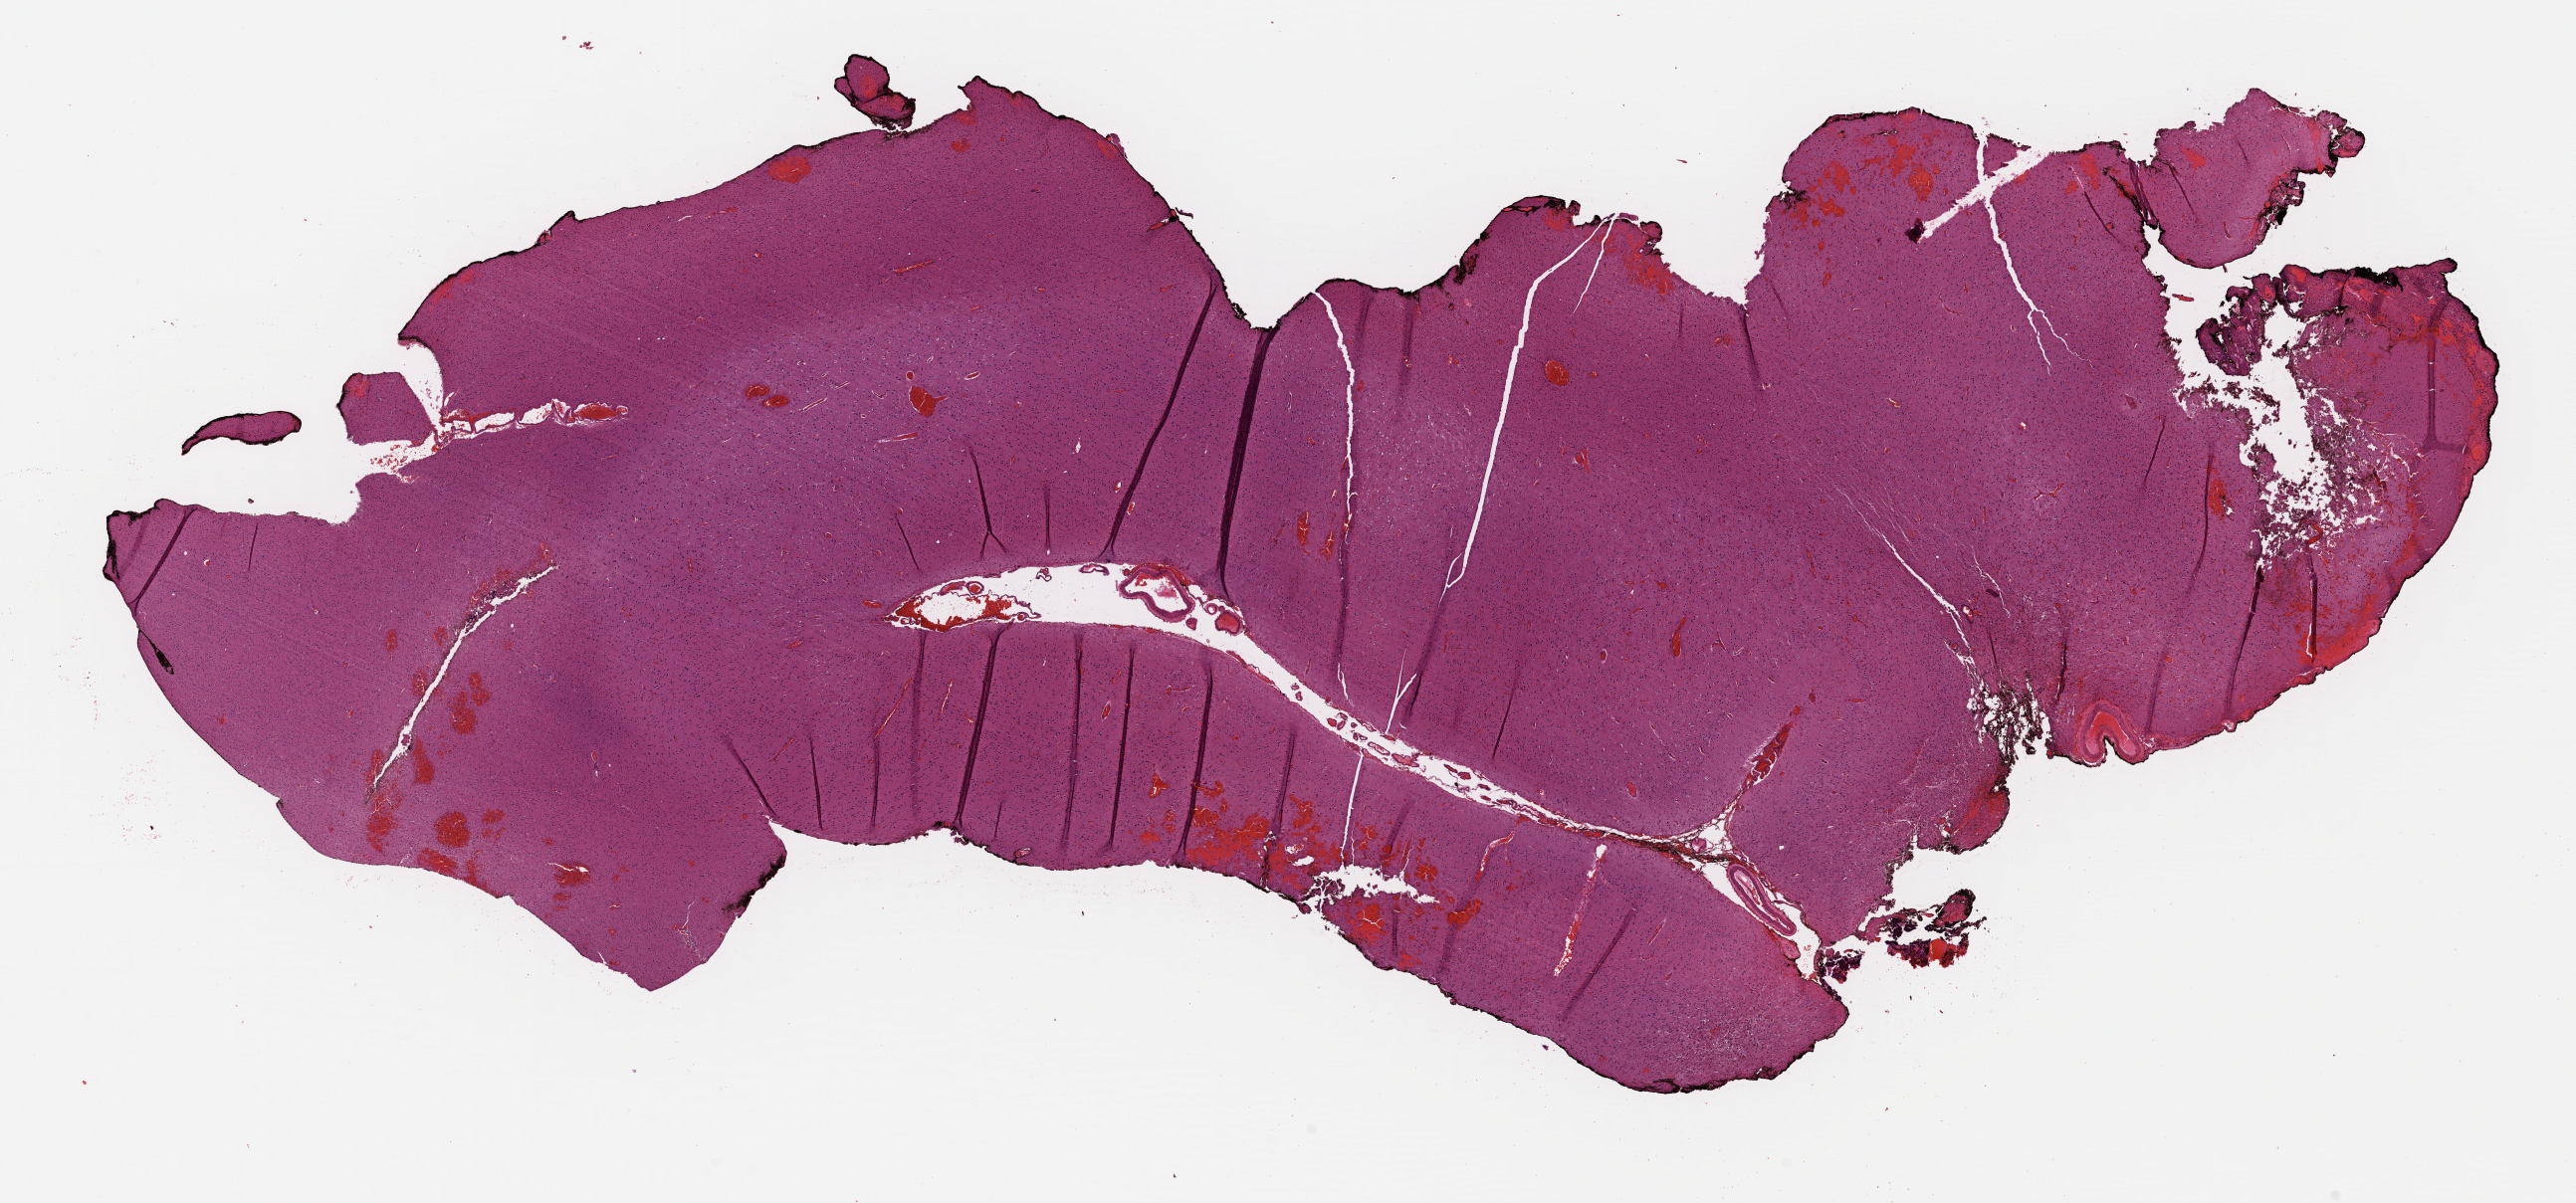
Digitized H&E-stained tissue section (whole slide), whole scanned area (about 20.3 x 9.5 mm) shown as a low-resolution overview; formalin-fixed paraffin-embedded (FFPE) diagnostic section; sample: primary tumour, brain. Female, age 61 years at initial diagnosis. Histologic grade: G2 (moderately differentiated).
Diagnosis: Astrocytoma, NOS (cerebrum). Laterality: left.